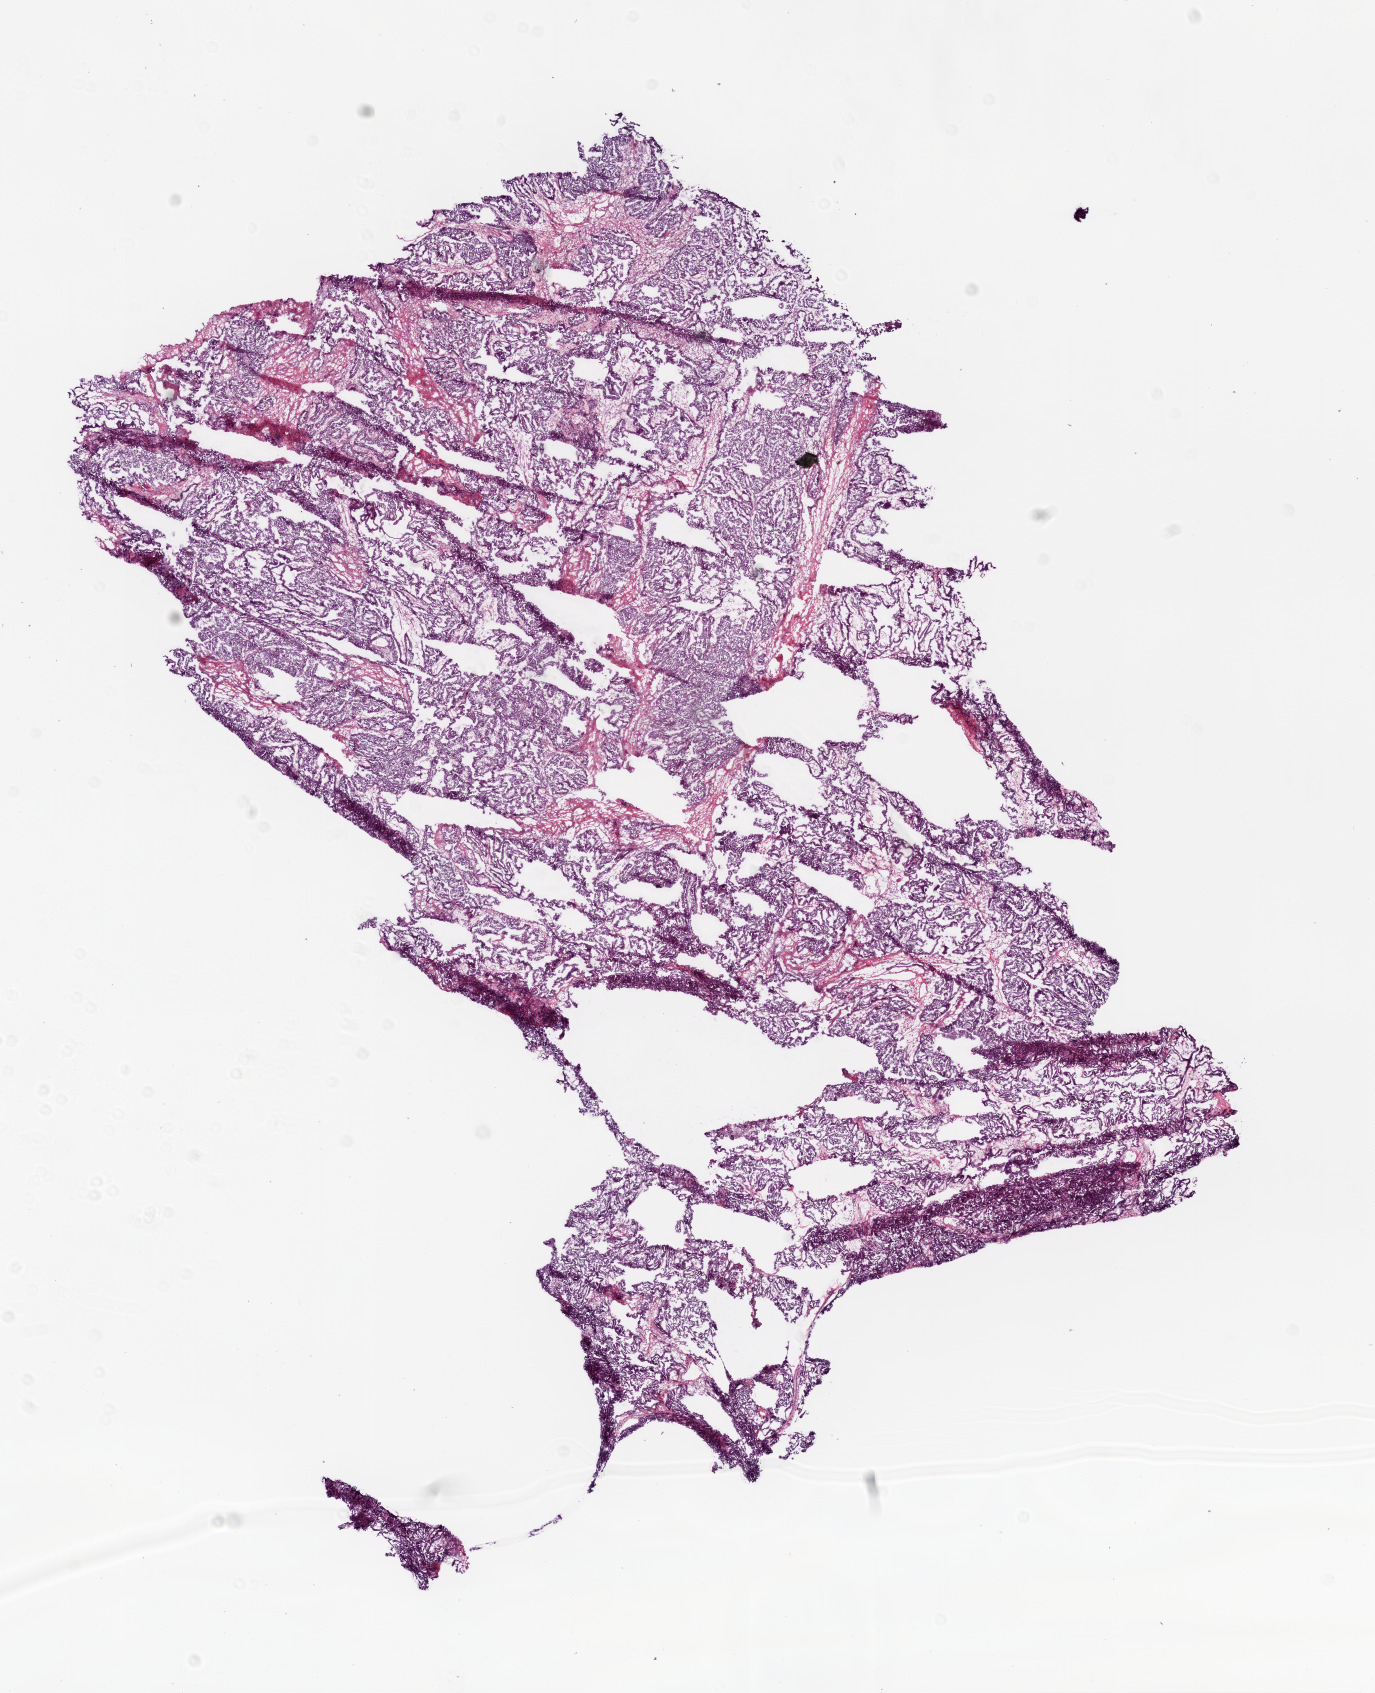
Whole-slide histology image, Hematoxylin and eosin (H&E) stained — shown as a low-resolution overview of the whole scanned area (about 11.0 x 13.6 mm). Frozen section from the bottom of the tissue portion. Sample: primary tumour, ovary. Female patient; age at initial diagnosis 64 years. Histologic grade: G3 (poorly differentiated). Composition of this section per pathologist review: tumour cells 90%, tumour nuclei 90%, normal cells 0%, stromal cells 10%, necrosis 0%. Infiltration values recorded for this section: lymphocyte infiltration 0%, monocyte infiltration 0%, neutrophil infiltration 0%.
• diagnosis: Serous cystadenocarcinoma, NOS
• FIGO stage: IIIC
• laterality: bilateral